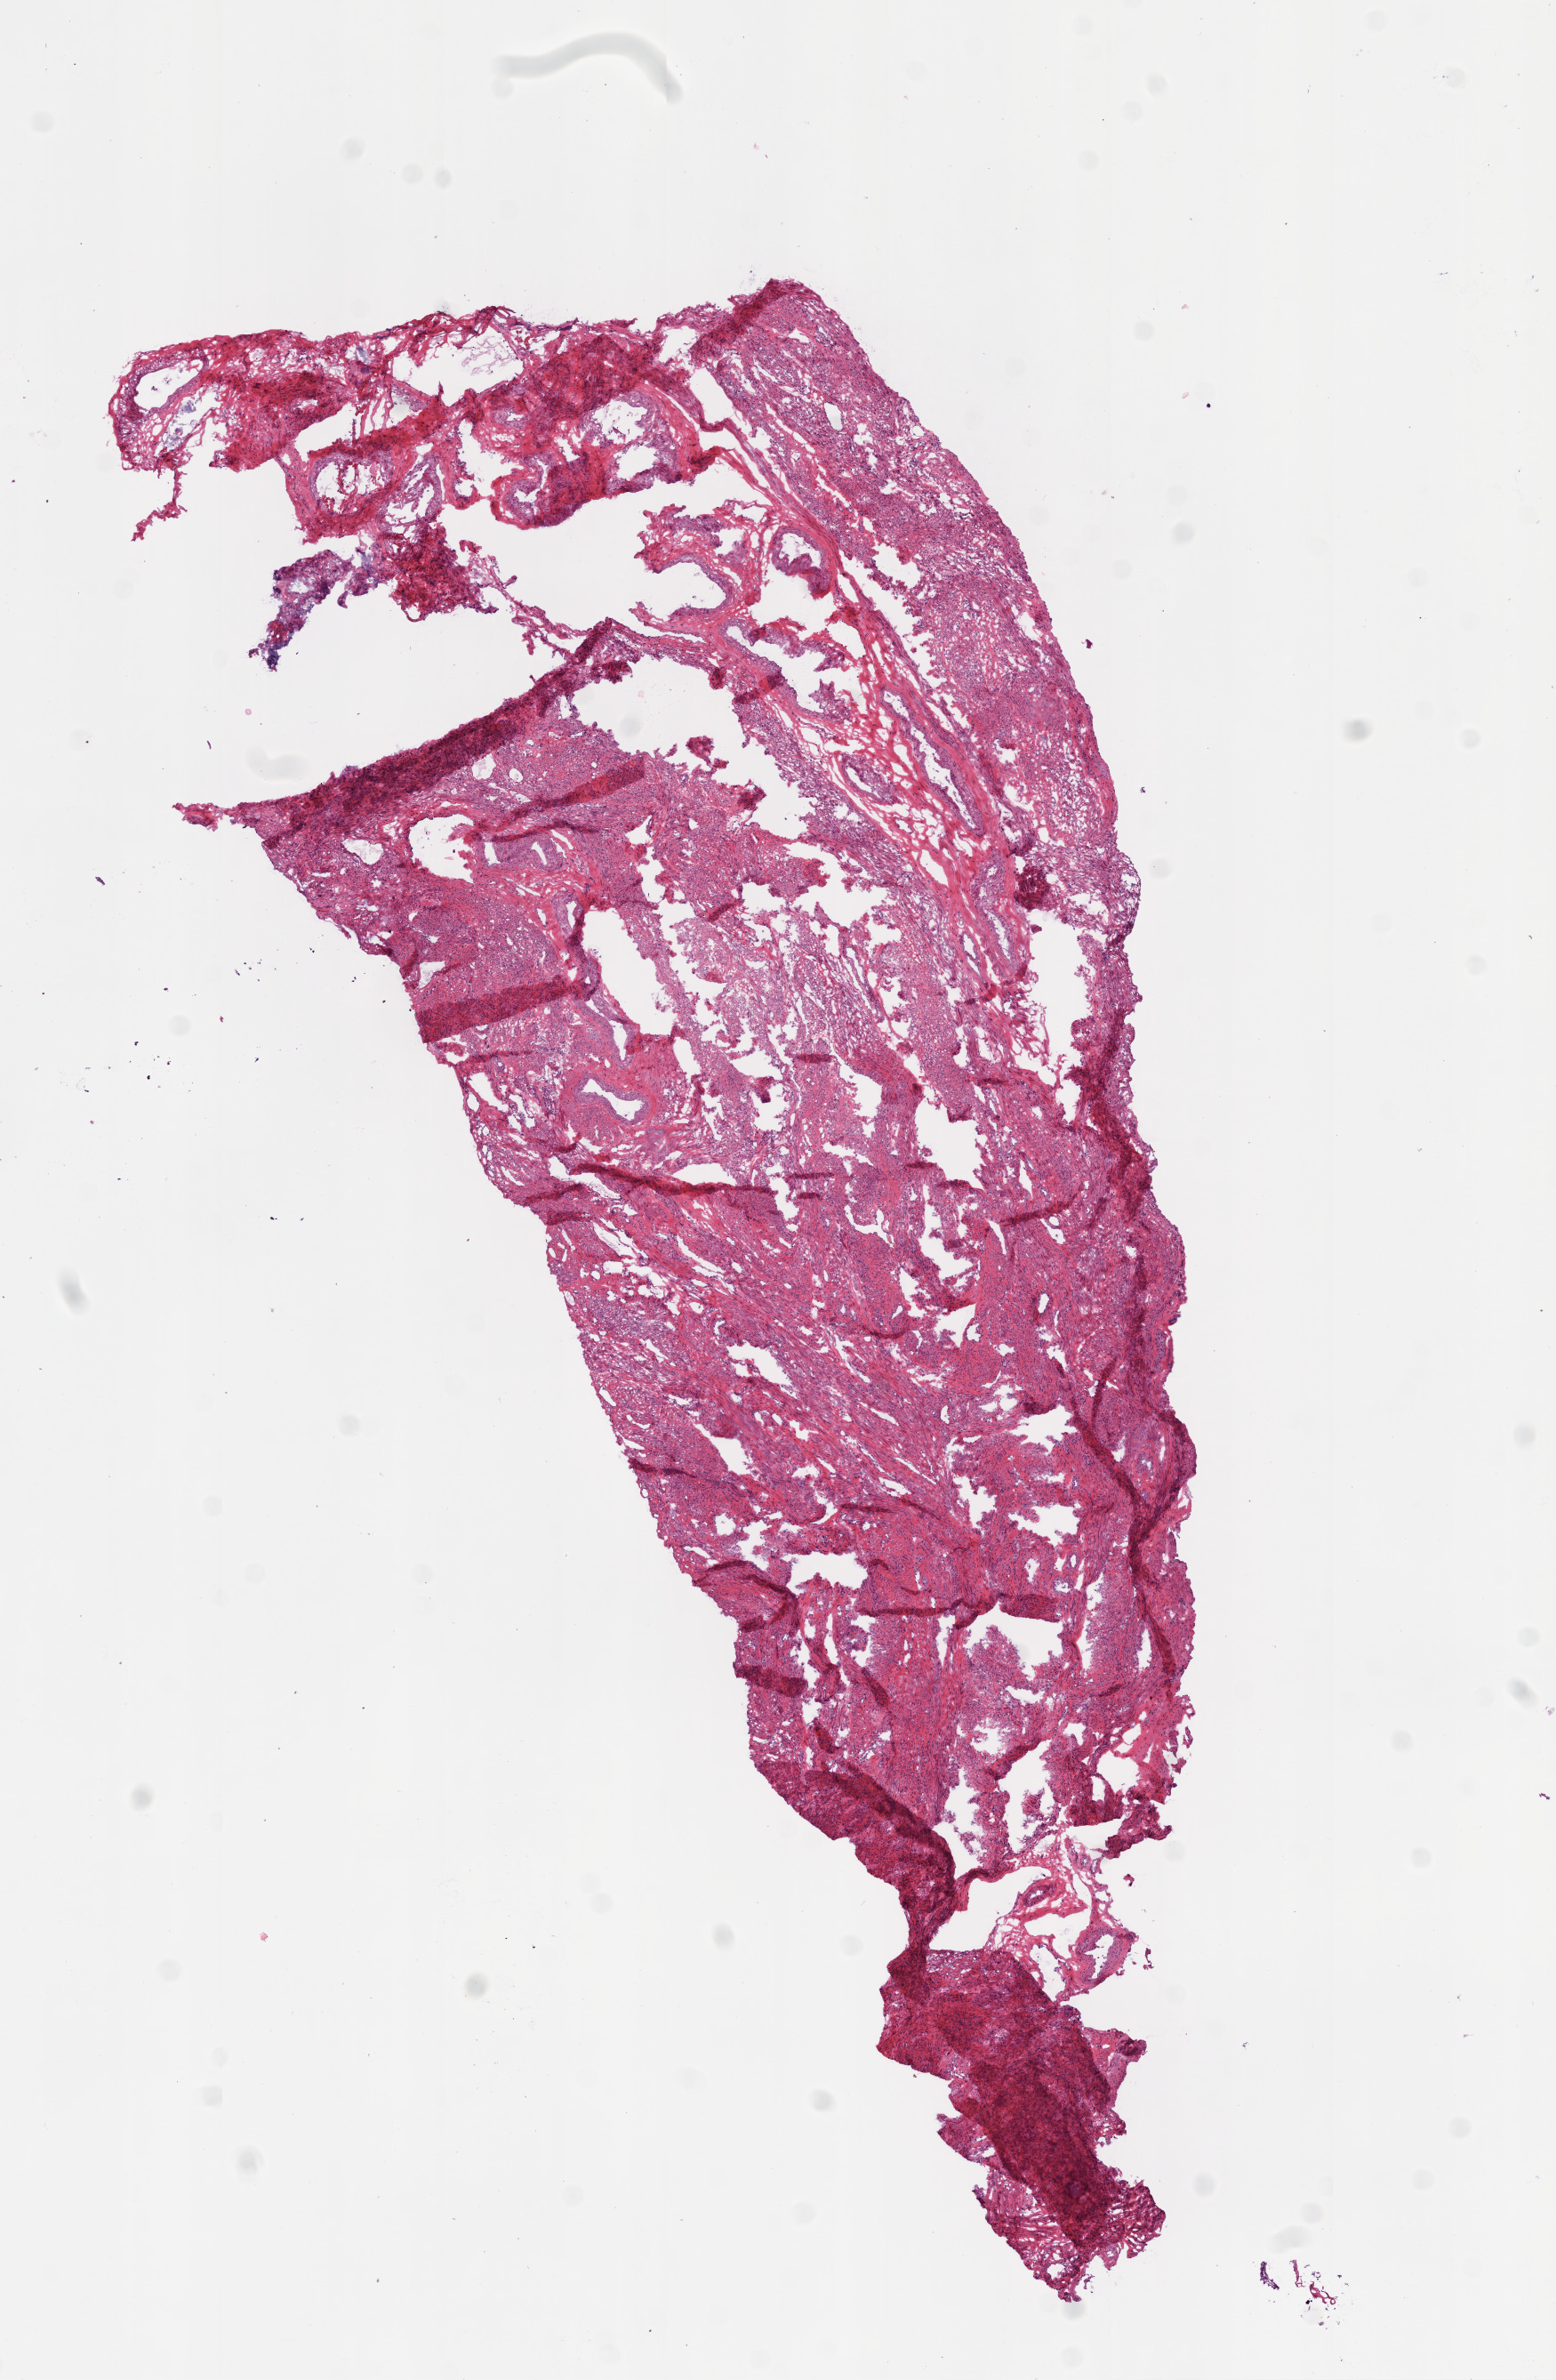
Whole-slide histology image, H&E, whole scanned area (about 7.0 x 10.7 mm) shown as a low-resolution overview. Frozen section from the top of the tissue portion. Solid tissue normal (non-tumour tissue) sample from the ovary. Patient: female, age at initial diagnosis 52 years.
This section: solid tissue normal sample (biorepository sample class). Patient diagnosis: Serous cystadenocarcinoma, NOS.